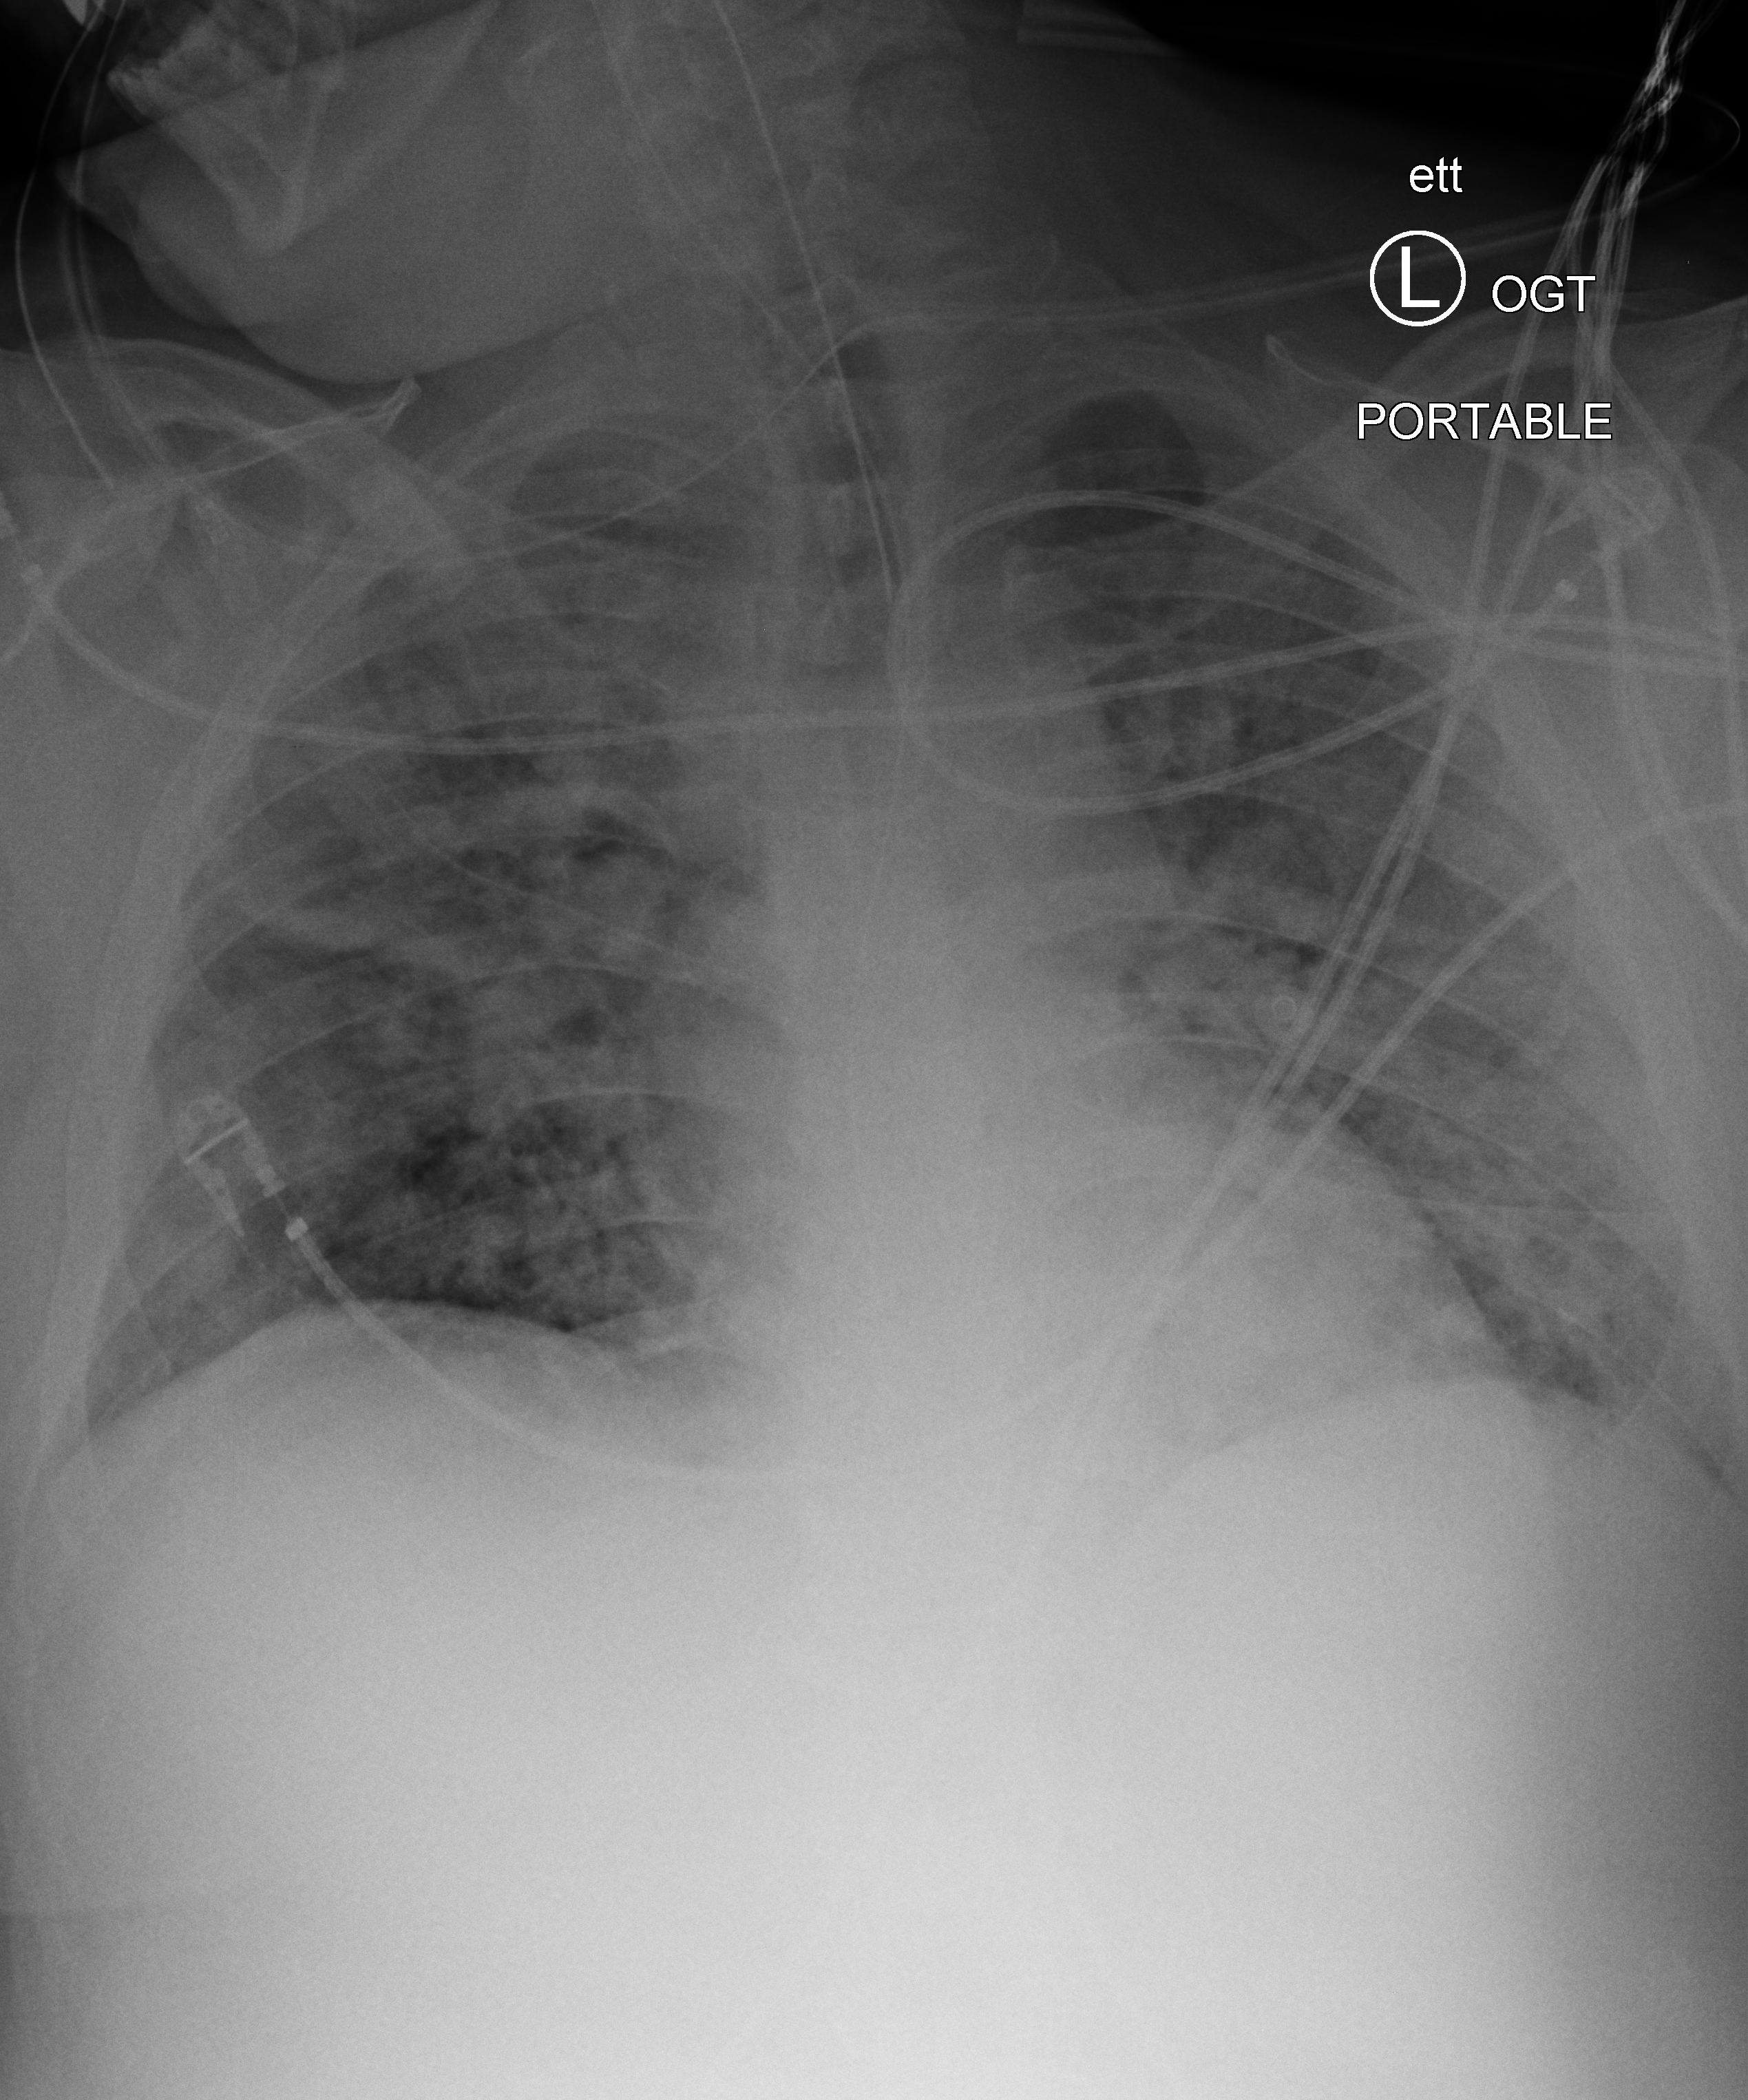
Chest X-ray (portable), anteroposterior (AP) projection. Adult patient hospitalised with COVID-19, age 18–59 years.
Hospital-stay facts (about this admission, not read from this image; timing relative to this image not recorded): mechanically ventilated during this hospital stay: yes.